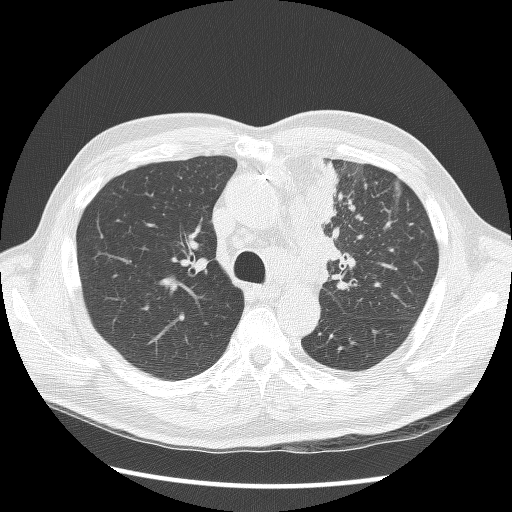
Chest CT (low-dose screening protocol), one axial image; second screening round (one year after baseline); lung window (W 1500 / L -600 HU); 2.5 mm slice thickness; 120 kVp; slice 41 of 136 in the series. Male, age 64 years at enrolment. Former smoker at enrolment.
- Expert-annotated lung lesion, box from (x=298, y=165) to (x=371, y=290) px.
- No non-calcified nodule or mass ≥4 mm was recorded by the screening reader at this exam.
- Lung cancer was diagnosed 24 days after this screen: small cell carcinoma, NOS, left upper lobe, stage IV (AJCC 6th edition), 100 mm at pathology.